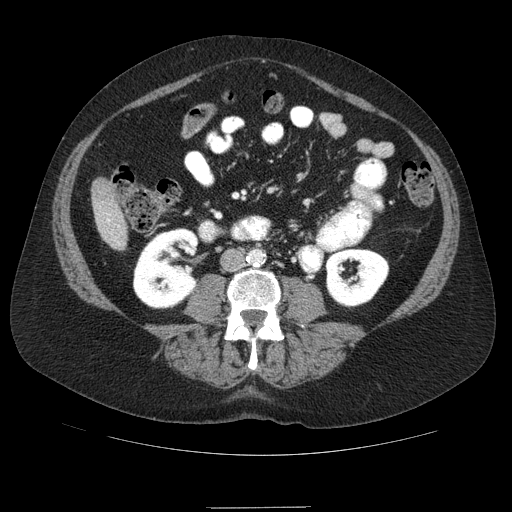
Contrast-enhanced abdominal CT (liver protocol), one axial slice; slice 14 of 89 in the series (ordered by position); reconstruction kernel STANDARD; 120 kVp; soft-tissue window (W 400 / L 40 HU); 512 × 512 image matrix. Case-level facts recorded for this patient, not image findings: diagnosis: hepatocellular carcinoma (patient treated with transarterial chemoembolisation; whether this scan precedes or follows treatment is not stated here); TNM stage (as recorded): Stage-IIIB; Child-Pugh class: A.
Annotated regions visible in this slice (semi-automatic segmentation, software-assisted and operator-edited):
- liver parenchyma outside the tumour (the mass and vessels are separate outlines, so this box may not span the whole liver): box from (x=92, y=178) to (x=126, y=250) px
- liver vessels: (x=107, y=219)–(x=110, y=222)